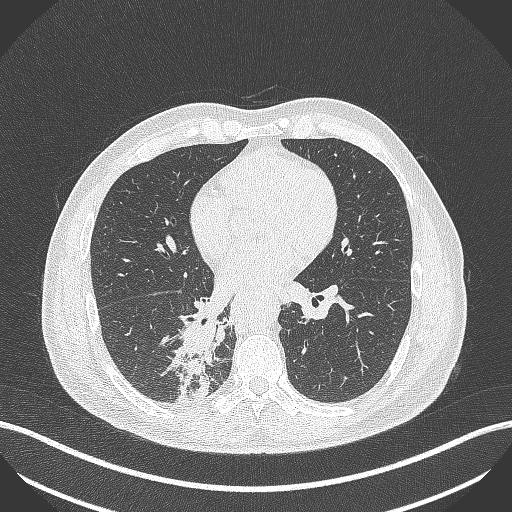
Chest CT, one axial slice; position 216 of 451 along the scan axis; lung window (W 1500 / L -600 HU); 1 mm slice thickness; 512 × 512 image matrix. Male patient, age 61 years. From the clinical record (not read from this slice): clinical TNM (as recorded): T1 N0 M0; histopathological grade: G3.
Structures marked on this image (rectangle marked by the reading radiologist):
- lung tumour (recorded histology: small cell carcinoma): box from (x=172, y=317) to (x=219, y=407) px